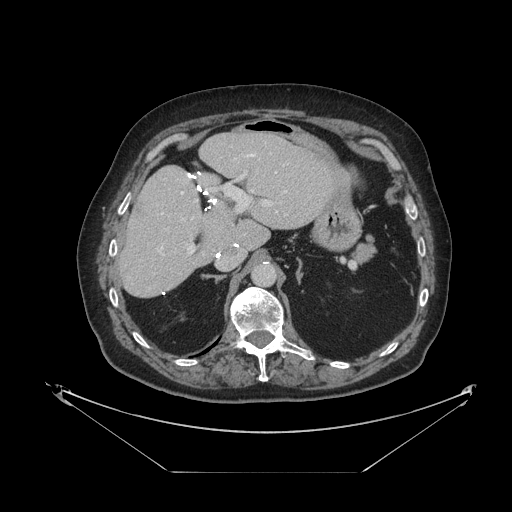
Contrast-enhanced abdominal CT, one axial slice; position 67 of 121 along the scan axis; 120 kVp; intravenous contrast given; soft-tissue window (W 400 / L 40 HU); 2.5 mm slice thickness; 512 × 512 image matrix. Male patient, age 68 years. From the clinical record (not read from this slice): diagnosis: colorectal cancer liver metastases, imaged before liver resection; multiple liver metastases: no; largest metastasis: 4 cm; disease in both lobes: no.
Outlined on this slice (manually delineated by an expert):
- hepatic veins: box from (x=159, y=154) to (x=286, y=255) px
- liver: (x=121, y=133)–(x=342, y=298)
- planned liver remnant (the part of the liver to remain after resection): (x=121, y=133)–(x=340, y=298)
- portal vein (with intrahepatic branches): (x=187, y=171)–(x=281, y=255)
- liver metastasis: (x=135, y=200)–(x=144, y=215)